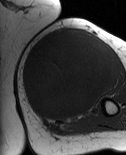
MRI of an extremity soft-tissue mass, one axial slice. MR volume resampled by the dataset authors to the PET/CT grid (not the native acquisition matrix). 3.27 mm slice thickness. 126 × 155 image matrix, field of view 123 × 151 mm. Female patient. Case-level facts recorded for this patient, not image findings: histological type: pleiomorphic leiomyosarcoma; grade: high; site of the primary tumour: left biceps.
Structures marked on this image (expert contour drawn on MRI and transferred to this co-registered scan by the dataset authors):
- gross tumour volume including surrounding oedema: bounding box (x1, y1, x2, y2) in pixels: (22, 28, 114, 121)
- gross tumour volume (mass): (22, 29, 114, 121)